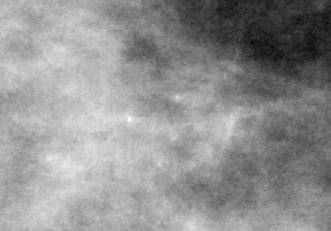
Crop from a digitized film mammogram around one marked abnormality, left breast, CC view.
- Marked abnormality: calcifications, morphology pleomorphic, distribution clustered; BI-RADS assessment category 4; subtlety rating 1 on a 1 (subtle) to 5 (obvious) scale; pathology (as recorded): malignant.